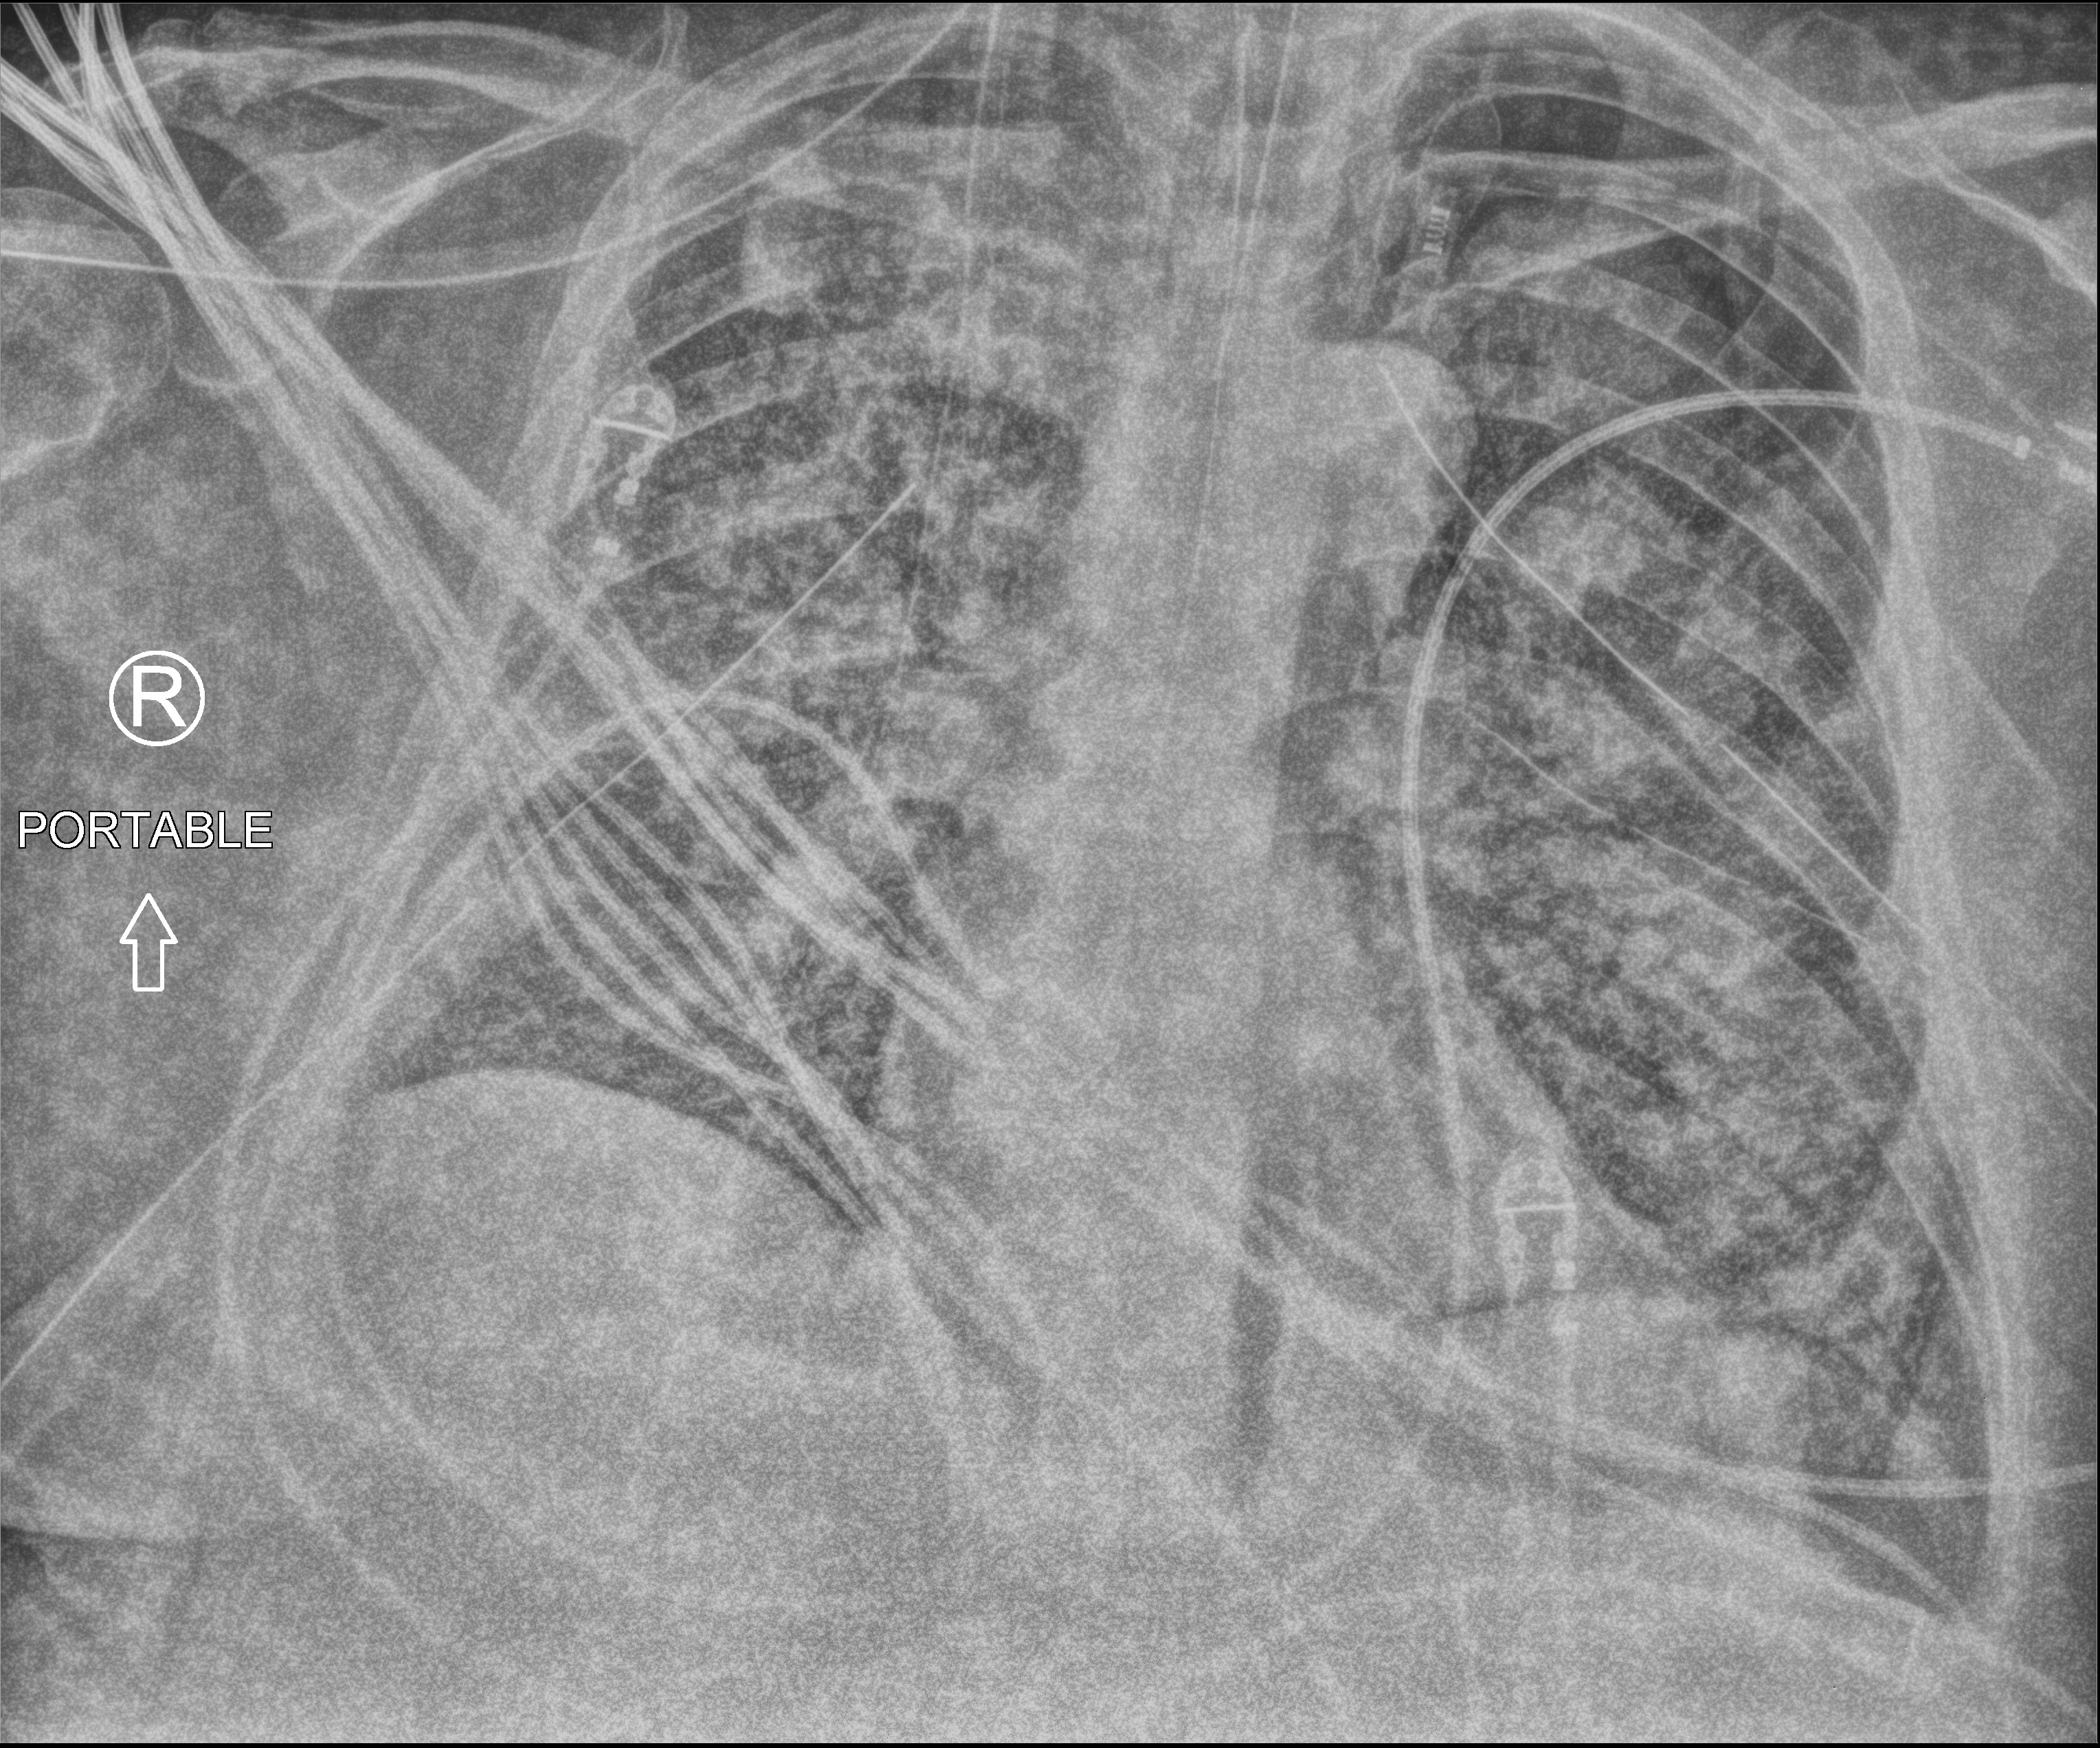
Portable chest radiograph, anteroposterior (AP) projection. Patient hospitalised with COVID-19, aged 18–59 years.
Hospital-stay facts (about this admission, not read from this image; timing relative to this image not recorded): length of hospital stay: 28 days; mechanically ventilated during this hospital stay: yes; COPD (admission record): no.